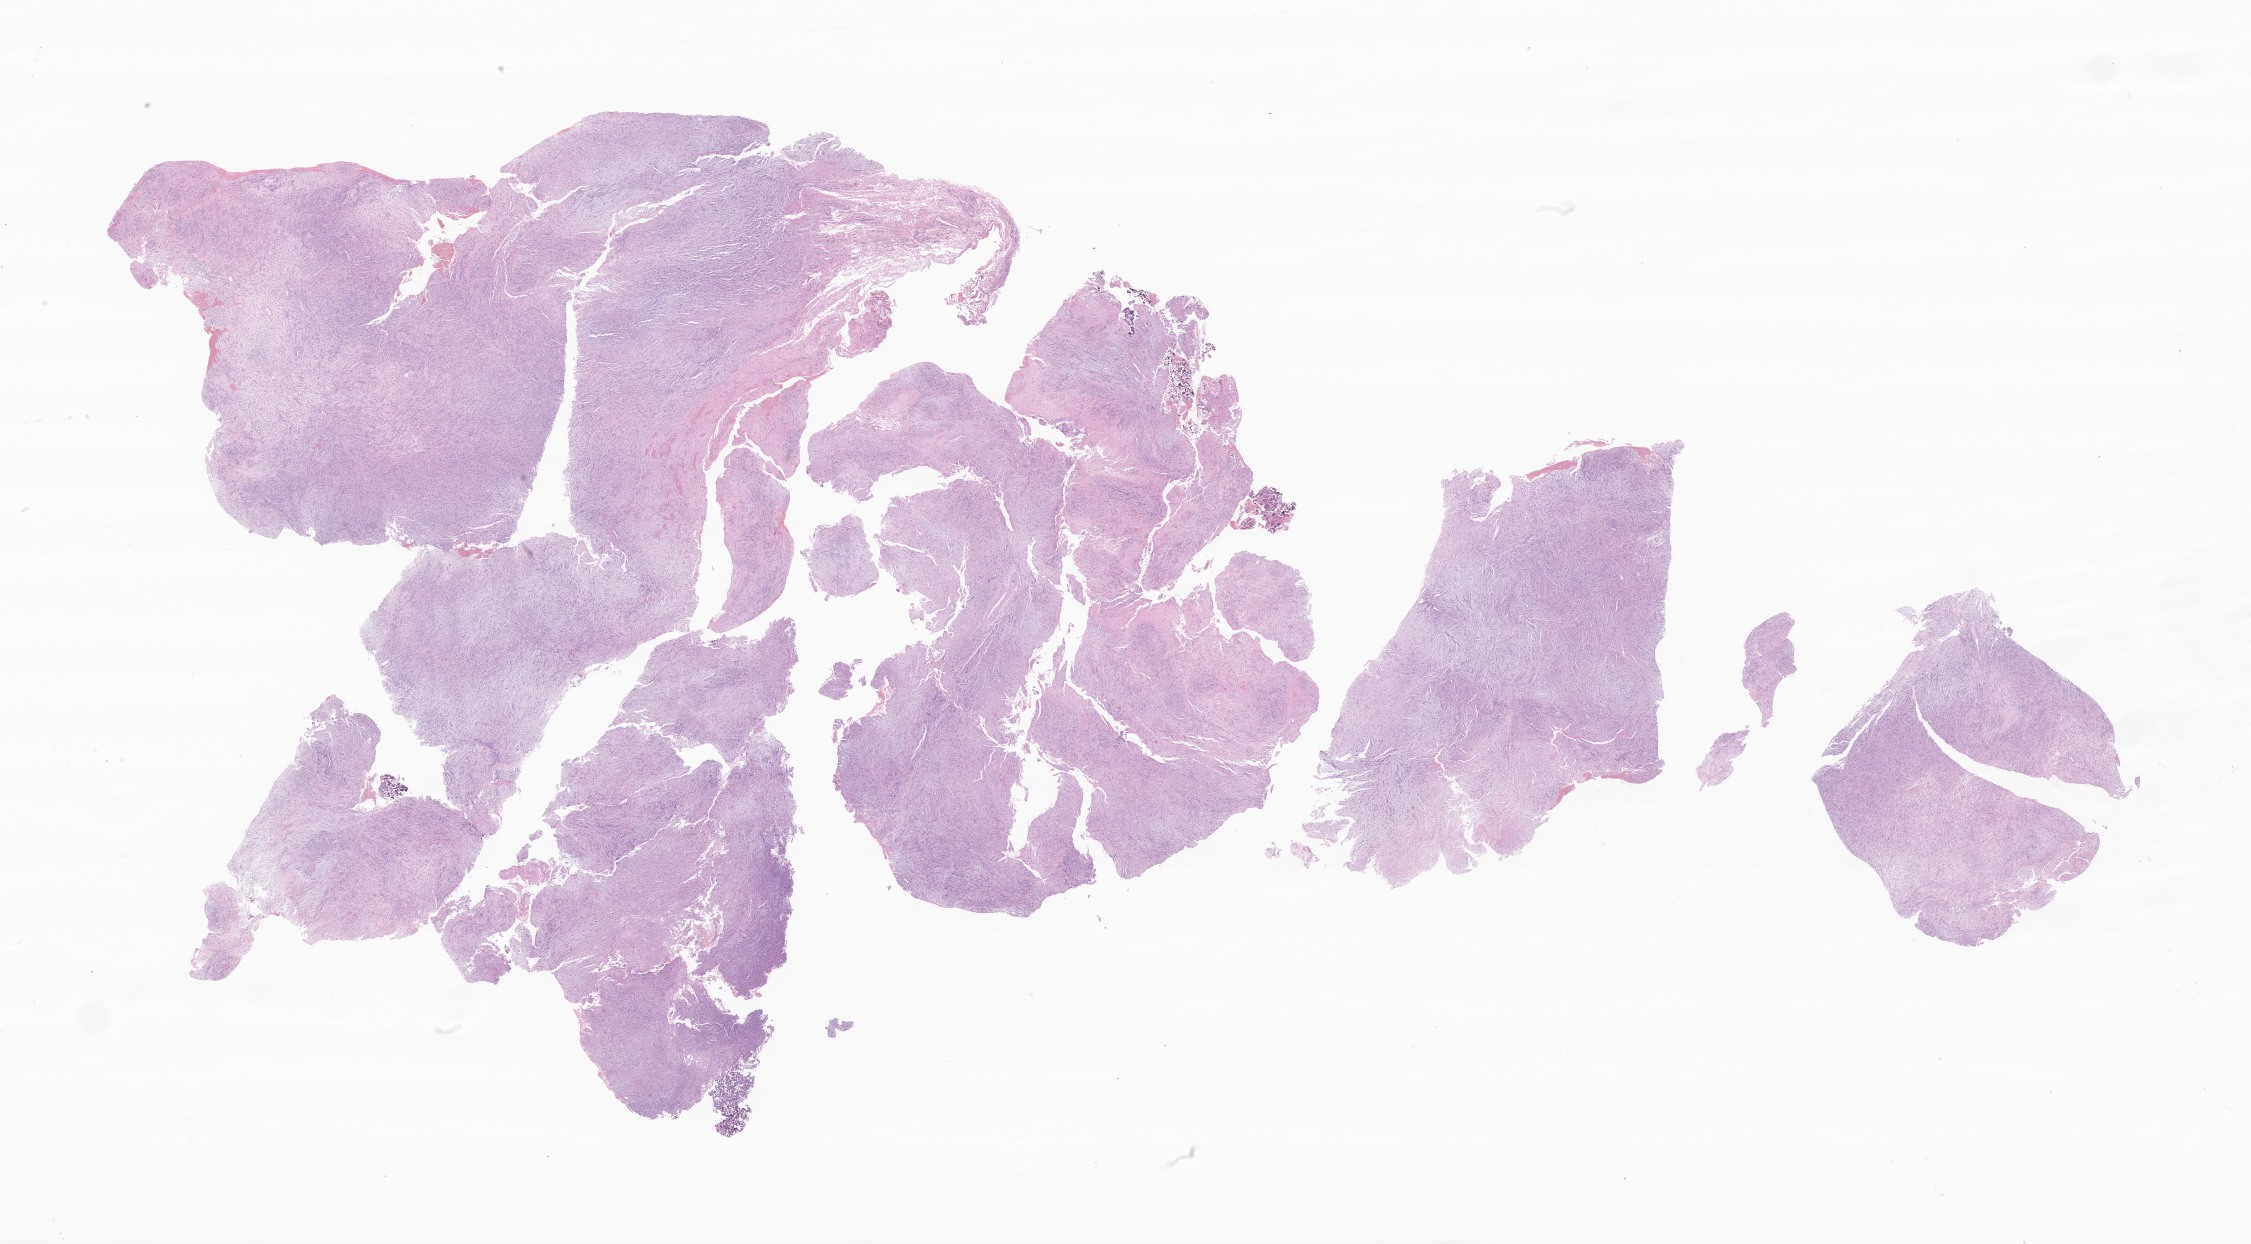
Whole-slide image, haematoxylin and eosin stain of tumor tissue from the head and neck, a low-resolution overview of the entire scanned area, about 38.0 x 21.0 mm. Formalin-fixed, paraffin-embedded (FFPE) tissue. Patient: male, age 200 months.
- diagnosis (ICD-O-3 morphology term): Spindle cell rhabdomyosarcoma
- tissue or organ of origin (case record): head, face or neck